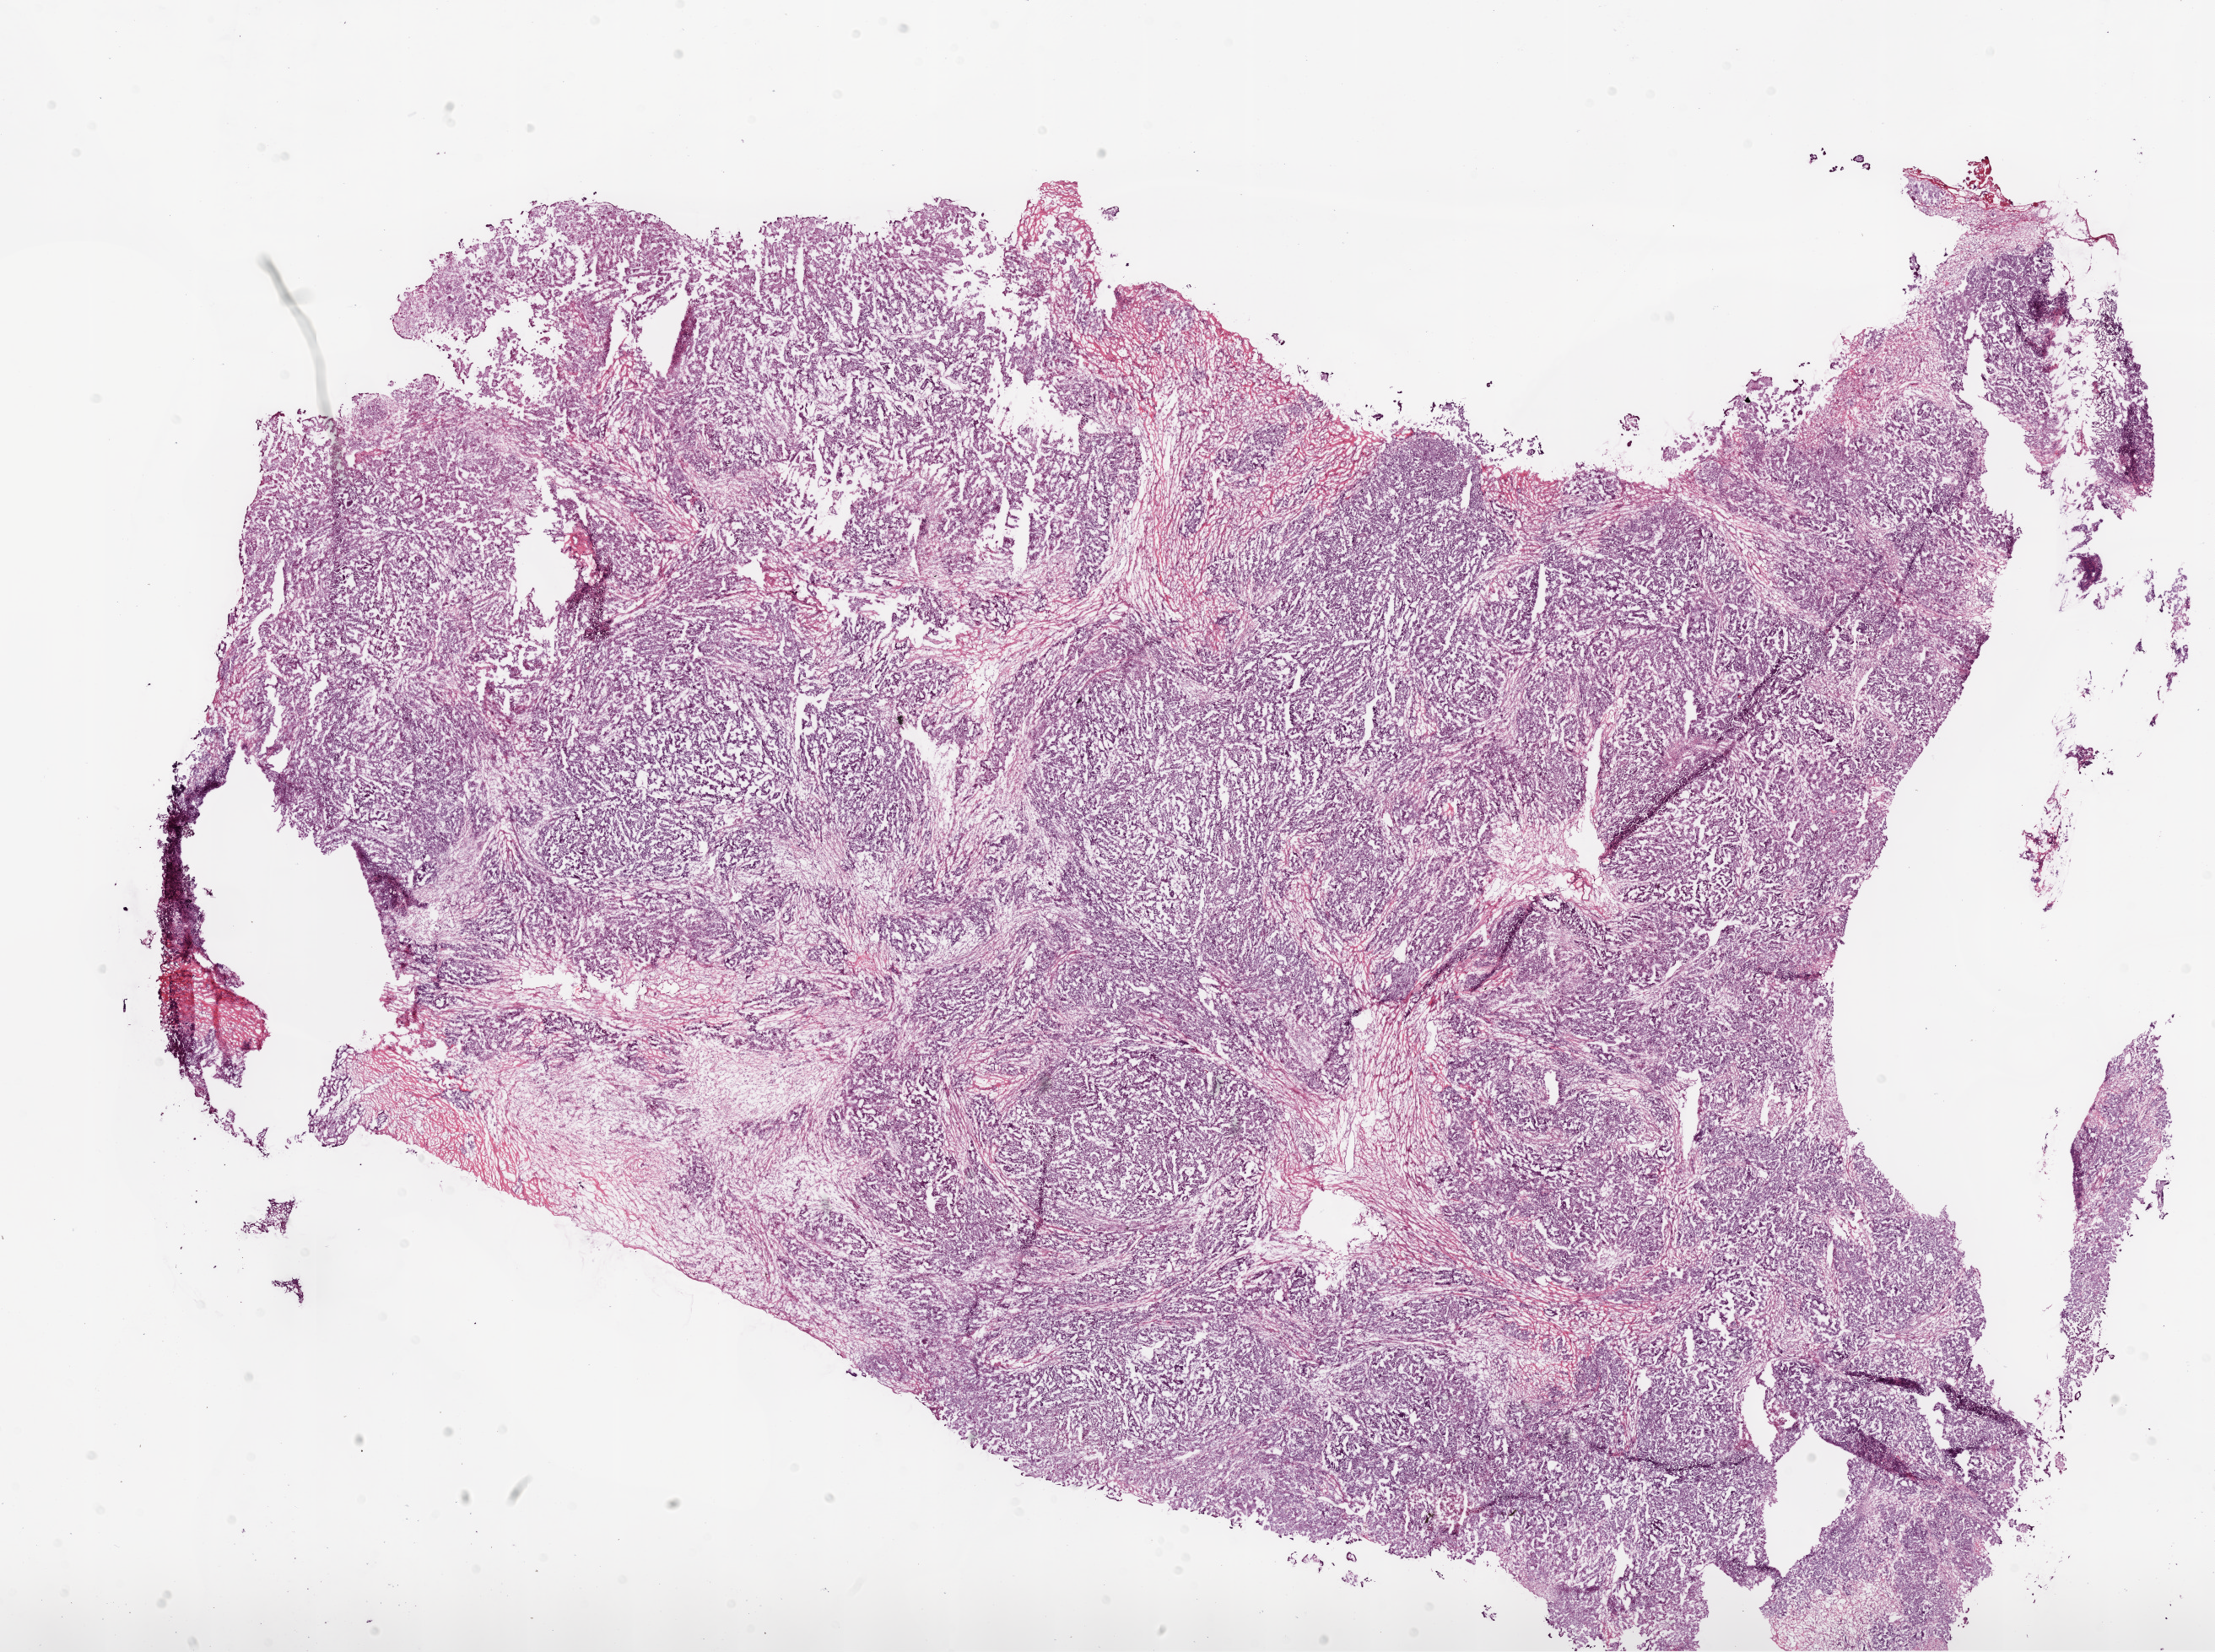
Digitized H&E-stained tissue section (whole slide), whole scanned area (about 21.1 x 15.7 mm, from a 20x scan) shown as a low-resolution overview. Frozen section. Sample: primary tumour, ovary. Female, age 47 years at initial diagnosis. Histologic grade: G2 (moderately differentiated). Composition of this section per pathologist review: tumour cells 85%, tumour nuclei 80%, normal cells 0%, stromal cells 0%, necrosis 15%.
Diagnosis: Serous cystadenocarcinoma, NOS. FIGO stage: IIIC.